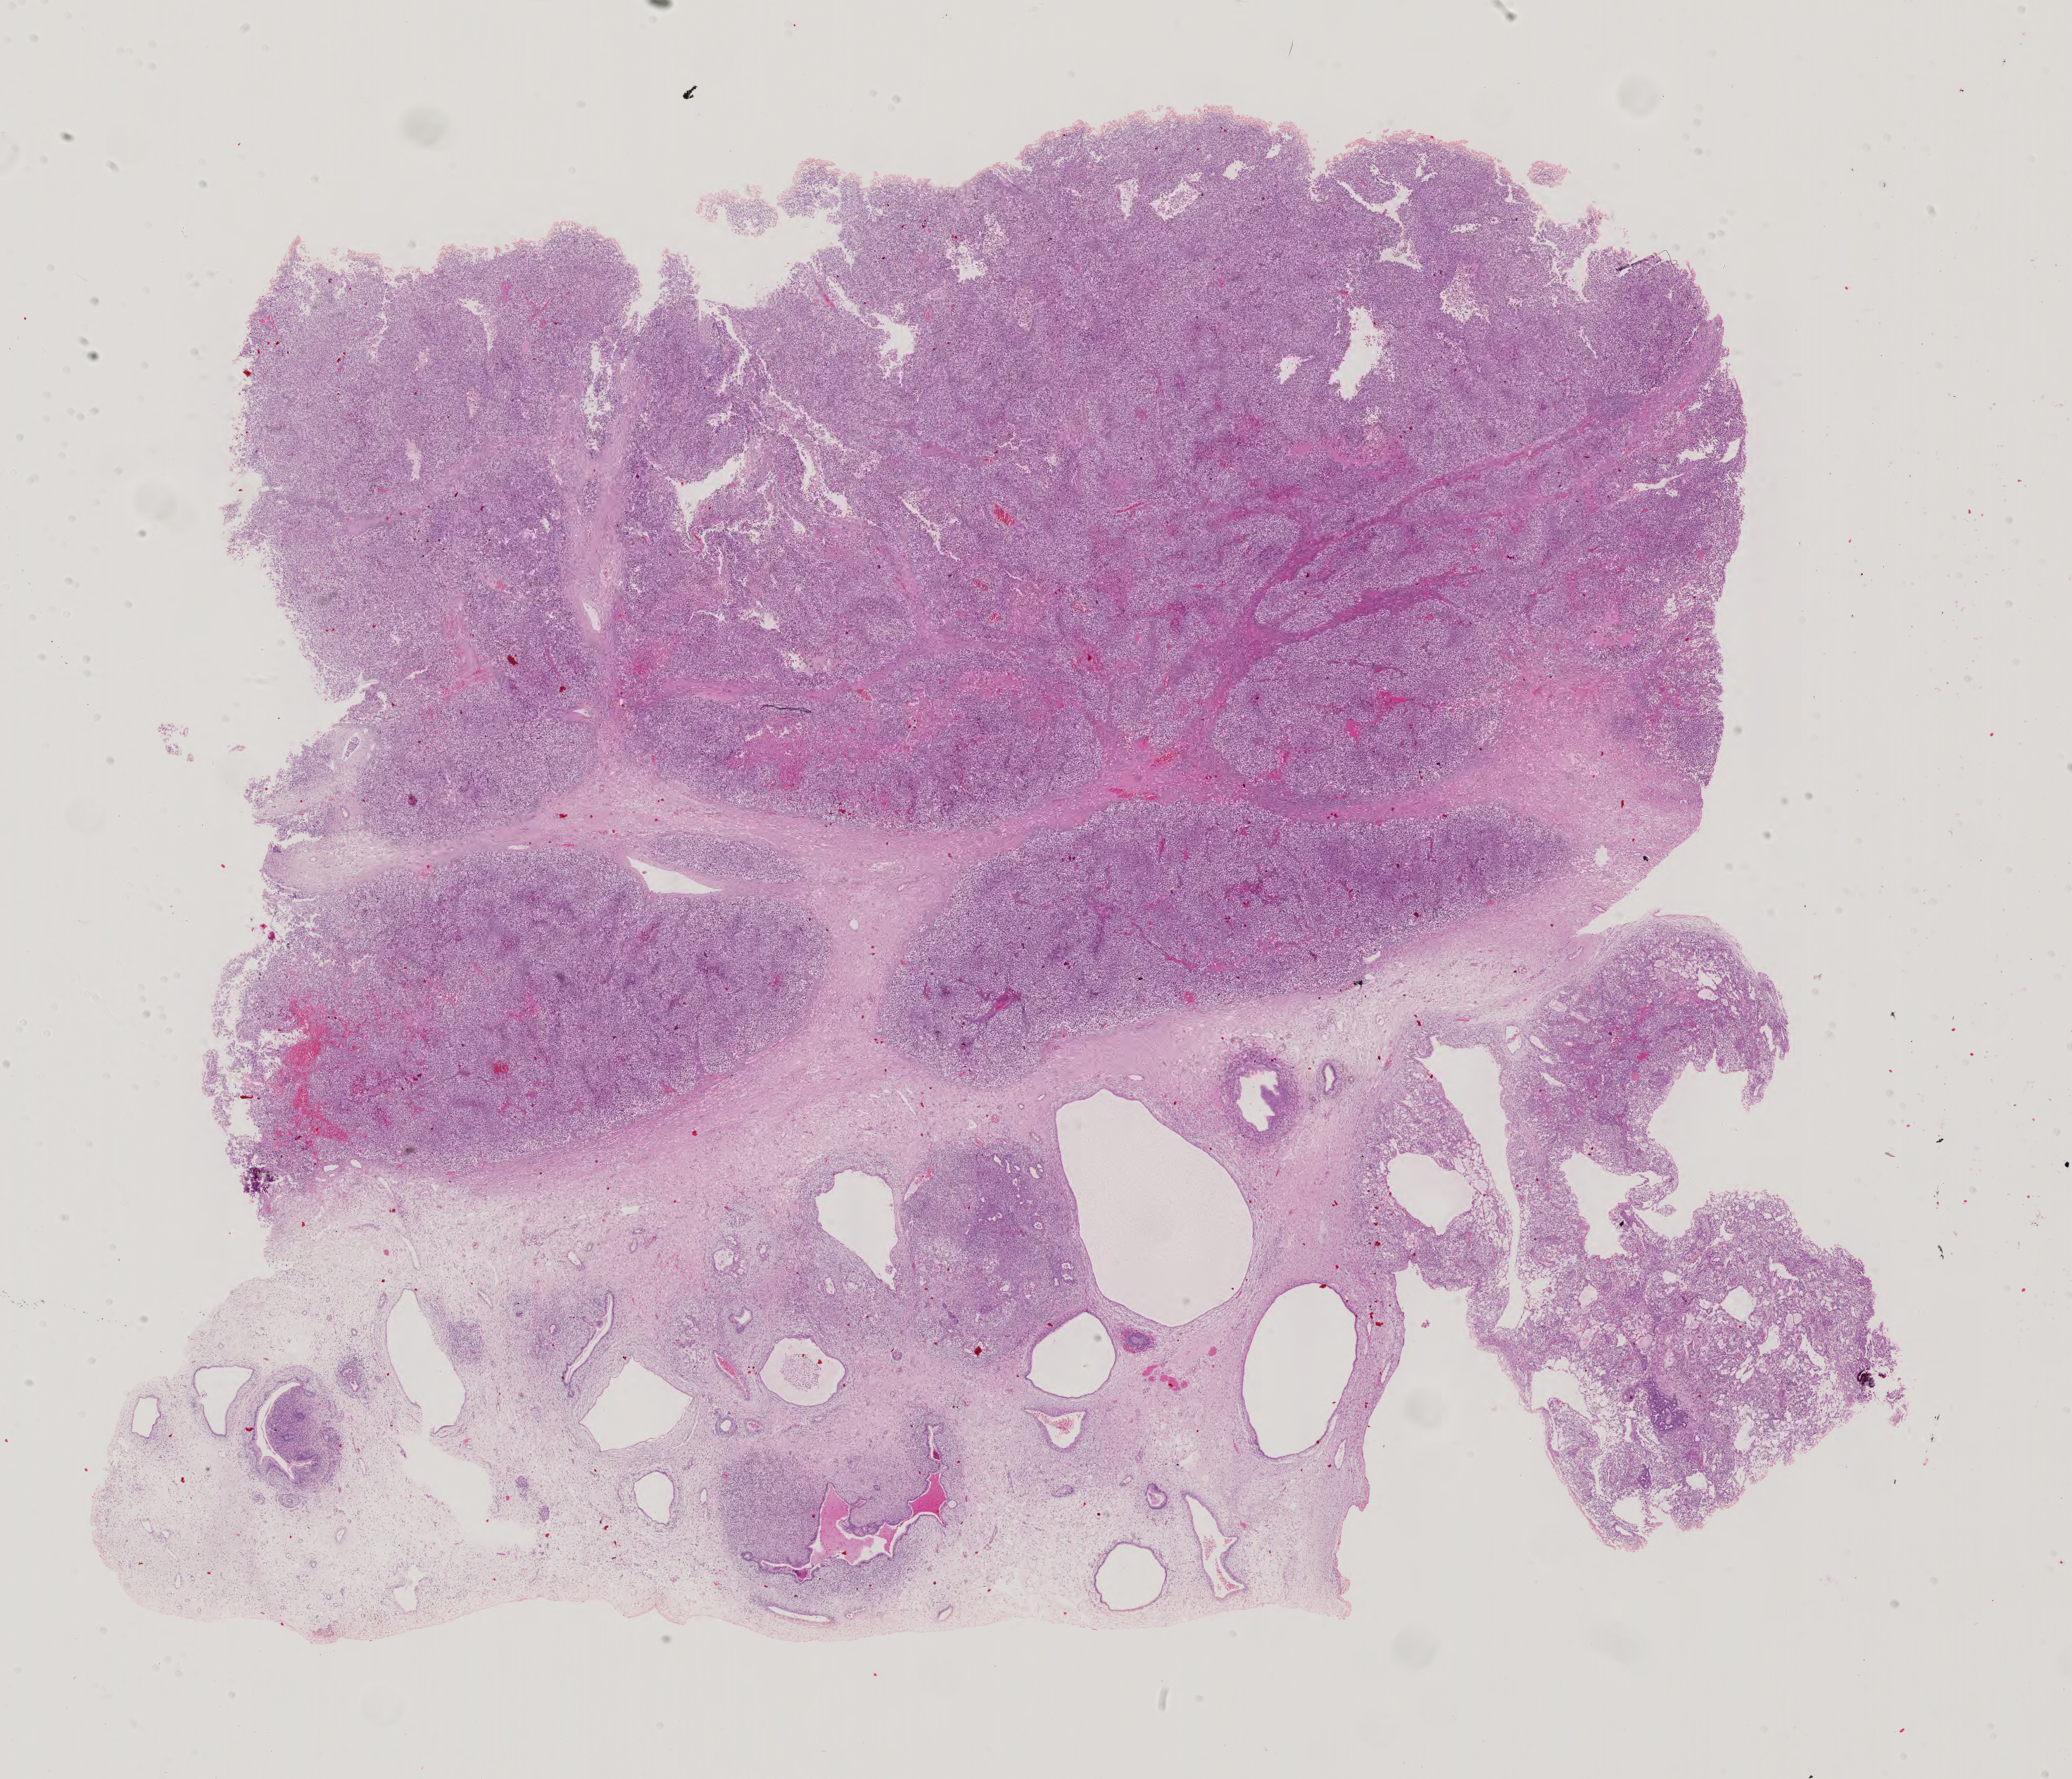
Digitized H&E-stained tissue section (whole slide), low-resolution overview of the scanned area, about 21.5 x 18.4 mm (acquisition: 40x scan). Male patient.
Specimen: formalin-fixed paraffin-embedded (FFPE) diagnostic section; sample: primary tumour, testis.